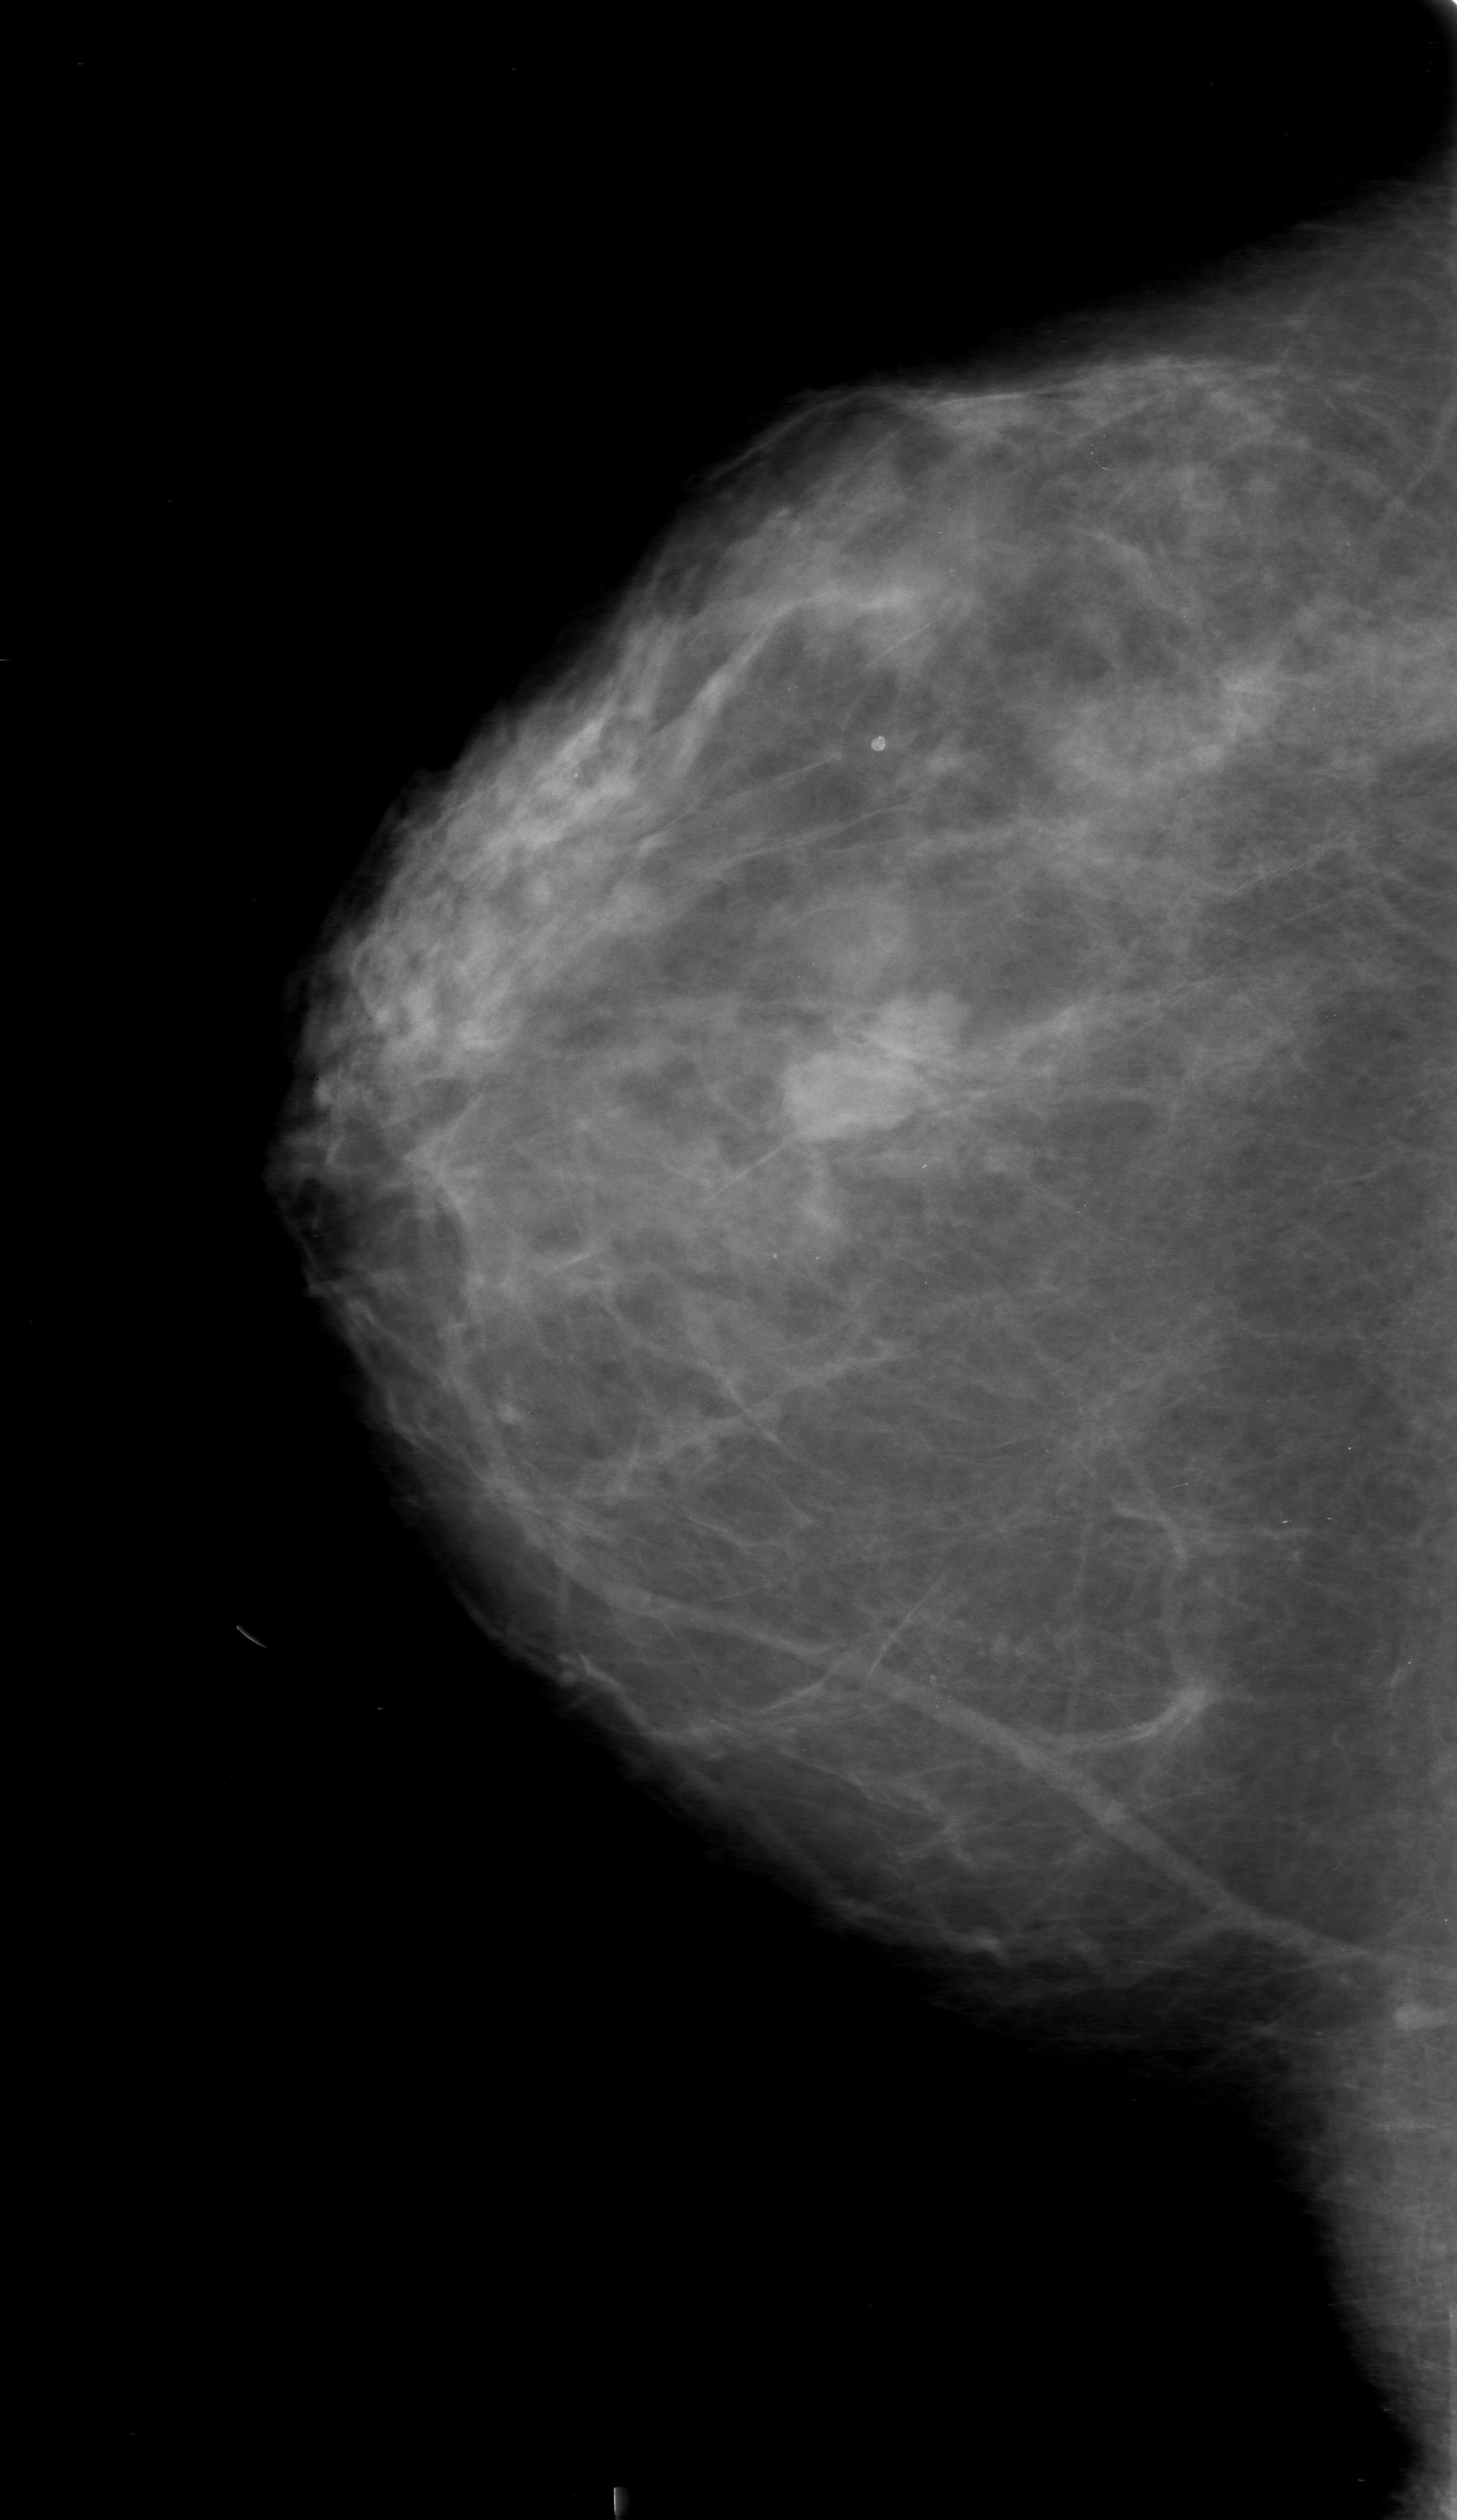
Scanned film-screen mammogram; right breast; CC view; BI-RADS breast density category 2 (scale 1–4).
- Radiologist-marked abnormalities on this image: mass, shape lobulated, margins obscured; BI-RADS assessment category 0 (incomplete: needs additional imaging); subtlety rating 5 on a 1 (subtle) to 5 (obvious) scale; pathology (as recorded): benign.